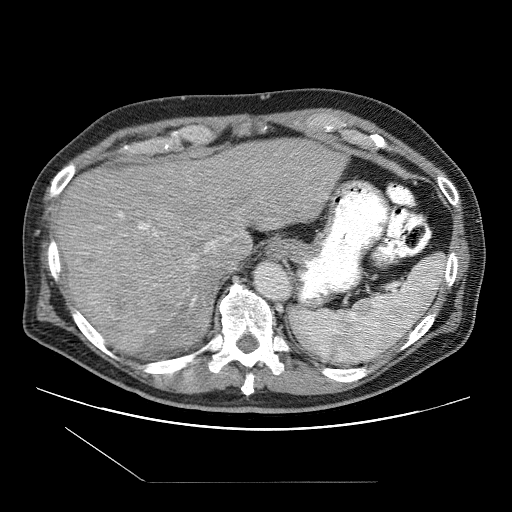
Contrast-enhanced abdominal CT (liver protocol), one axial slice; slice 77 of 109 in the series (ordered by position); reconstruction kernel STANDARD; one of 2 acquisitions stored at this slice position; soft-tissue window (W 400 / L 40 HU); 512 × 512 image matrix, field of view 400 × 400 mm. Case-level facts recorded for this patient, not image findings: diagnosis: hepatocellular carcinoma (patient treated with transarterial chemoembolisation; whether this scan precedes or follows treatment is not stated here); TNM stage (as recorded): Stage-IIIB; Child-Pugh class: A; tumour differentiation: well differentiated; tumour nodularity: multinodular.
Outlined on this slice (semi-automatically segmented with operator editing):
- liver parenchyma outside the tumour (the mass and vessels are separate outlines, so this box may not span the whole liver): bounding box [x1, y1, x2, y2] px = [54, 138, 344, 352]
- mass: [69, 230, 194, 353]
- liver vessels: [118, 212, 237, 305]